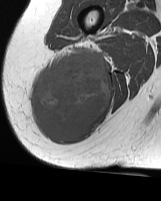
MRI of an extremity soft-tissue mass, one axial slice; position 23 of 70 along the scan axis; MR volume resampled by the dataset authors to the PET/CT grid (not the native acquisition matrix); 3.27 mm slice thickness; 161 × 201 image matrix. Female patient. Case-level facts recorded for this patient, not image findings: histological type: synovial sarcoma; grade: intermediate; site of the primary tumour: right buttock.
Structures marked on this image (expert contour drawn on MRI and transferred to this co-registered scan by the dataset authors):
- gross tumour volume including surrounding oedema: bounding box [x1, y1, x2, y2] px = [33, 45, 112, 142]
- gross tumour volume (mass): [33, 52, 112, 142]